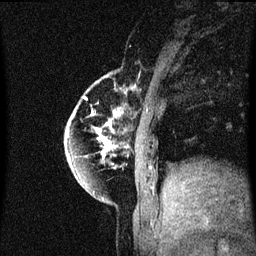
Breast MRI (dynamic contrast-enhanced), one sagittal slice. Slice 12 of 60 in the series (ordered by position). Dynamic contrast-enhanced series, image 2 of 3 at this slice position (ordered by acquisition). 1.5 T. TE 4.2 ms, TR 8.4 ms. 256 × 256 image matrix. Female patient, age 60 years.
Structures marked on this image (semi-automatic segmentation, software-assisted and operator-edited):
- analysis volume of interest (the breast-tissue region the enhancement analysis was run in; not a lesion): bounding box [x1, y1, x2, y2] px = [64, 82, 127, 195]
- tumour enhancement mask (voxels above the 70 % enhancement threshold inside the analysis volume of interest): [66, 112, 119, 169]